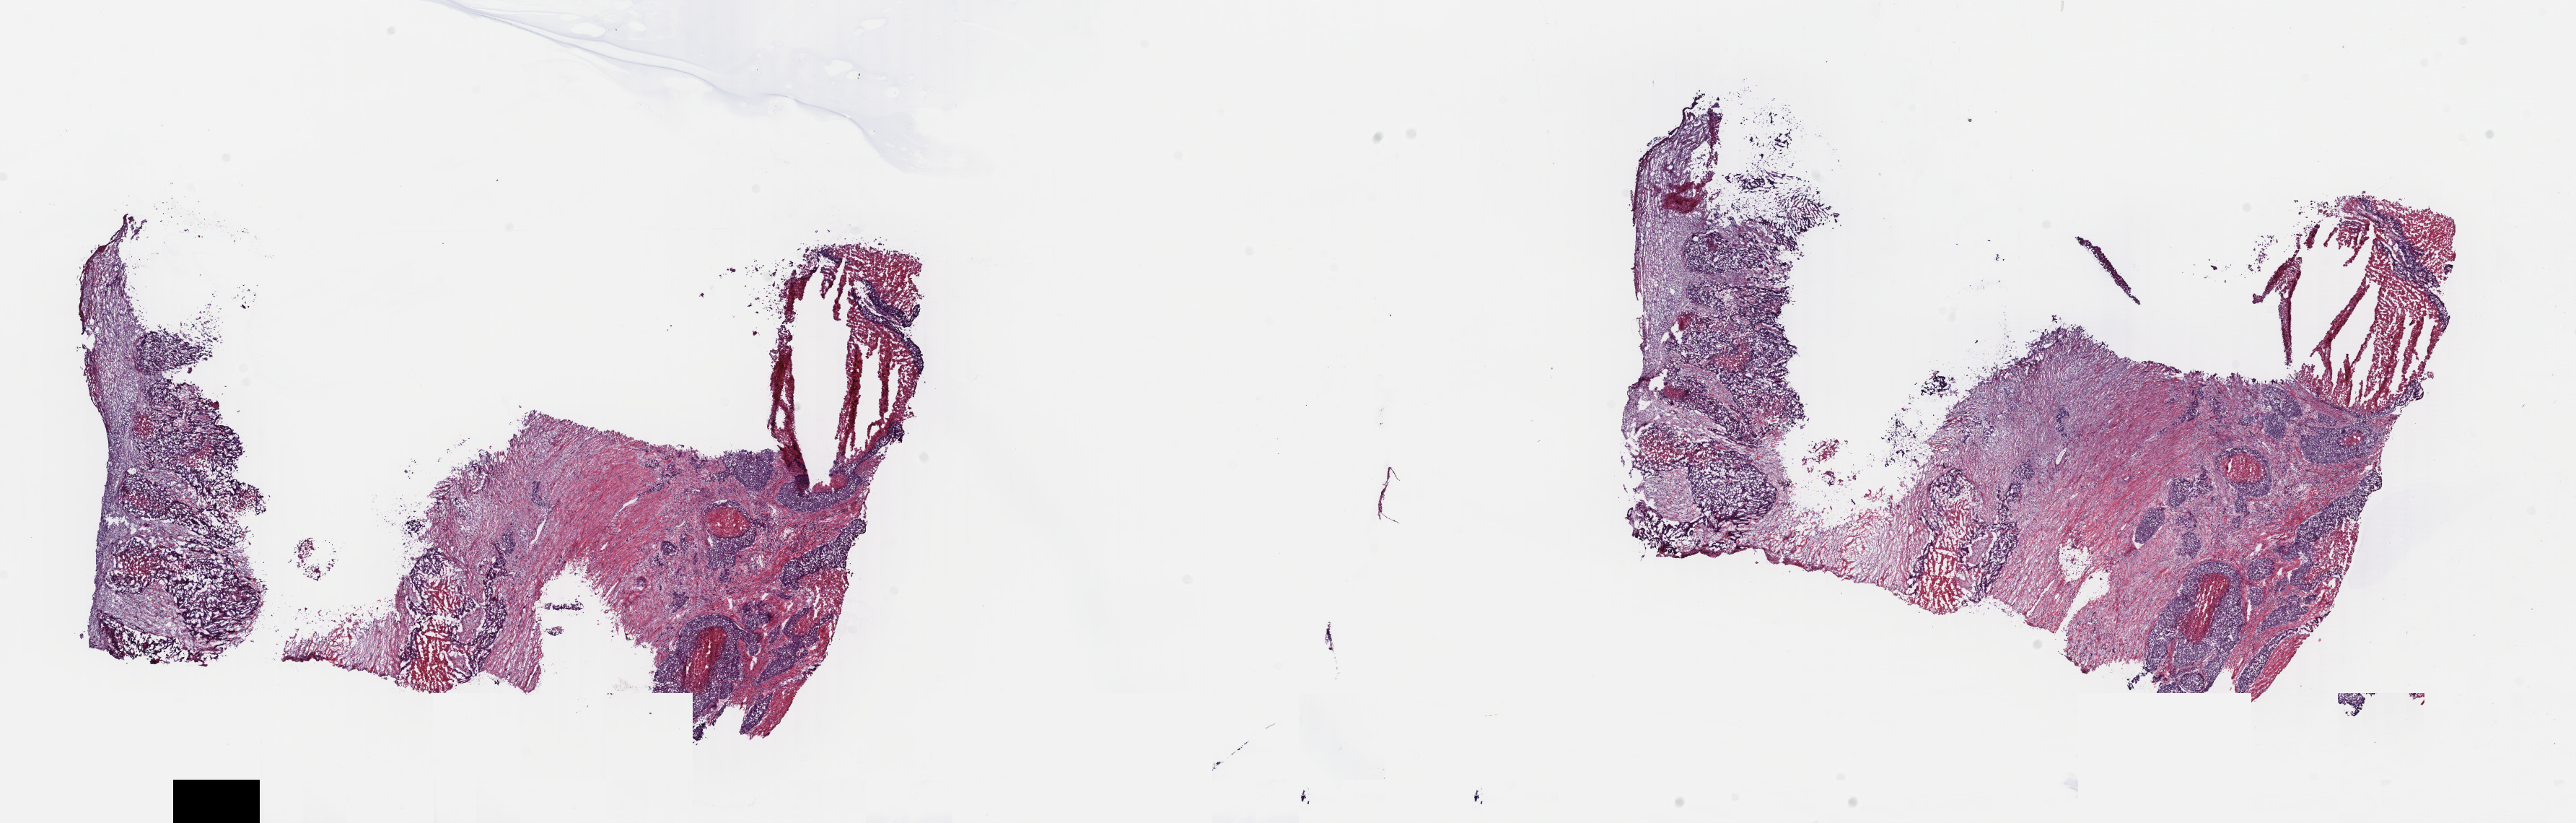
Whole-slide histology image, H&E-stained — shown as a low-resolution overview of the whole scanned area (about 28.2 x 9.0 mm), frozen section from the top of the tissue portion, sample: primary tumour, lung. Patient: female, age at initial diagnosis 45 years. Slide review estimates, as recorded: tumour cells 25%, tumour nuclei 70%, normal cells 0%, stromal cells 55%, necrosis 20%. Infiltration values recorded for this section: lymphocyte infiltration 5%, monocyte infiltration 0%, neutrophil infiltration 0%.
Laterality: right. TNM: T3 N0 M0. Pathologic diagnosis: Squamous cell carcinoma, NOS (upper lobe, lung). AJCC pathologic stage: IIB.